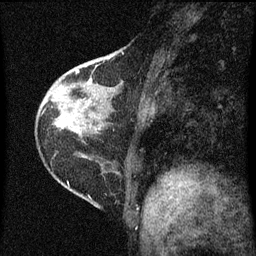
Breast MRI (dynamic contrast-enhanced), one sagittal slice. Position 22 of 60 along the scan axis. Dynamic contrast-enhanced series, image 2 of 3 at this slice position (ordered by acquisition). 1.5 T. TE 4.2 ms, TR 8 ms. 2 mm slice thickness. 256 × 256 image matrix, field of view 180 × 180 mm. Female patient, age 38 years.
Outlined on this slice (semi-automatically segmented with operator editing):
- analysis volume of interest (the breast-tissue region the enhancement analysis was run in; not a lesion): bounding box (x1, y1, x2, y2) in pixels: (67, 46, 139, 131)
- tumour enhancement mask (voxels above the 70 % enhancement threshold inside the analysis volume of interest): (76, 70, 79, 73)